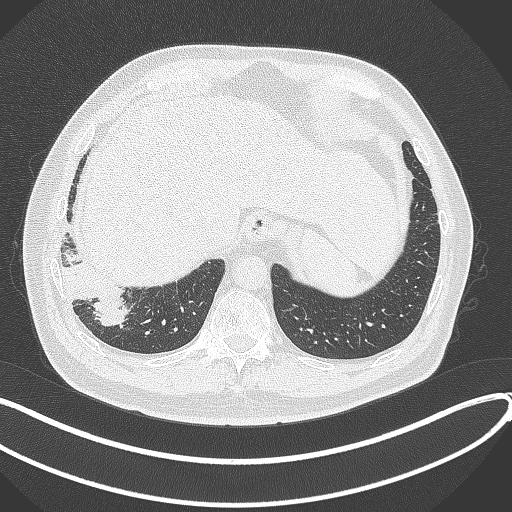
Chest CT, one axial slice. Position 59 of 360 along the scan axis. Reconstruction kernel B70f. 120 kVp. Lung window (W 1500 / L -600 HU). 1 mm slice thickness. 512 × 512 image matrix, field of view 400 × 400 mm. Patient: male, 59 years.
Outlined on this slice (rectangle marked by the reading radiologist):
- lung tumour (recorded histology: adenocarcinoma): bounding box (x1, y1, x2, y2) in pixels: (61, 260, 129, 327)